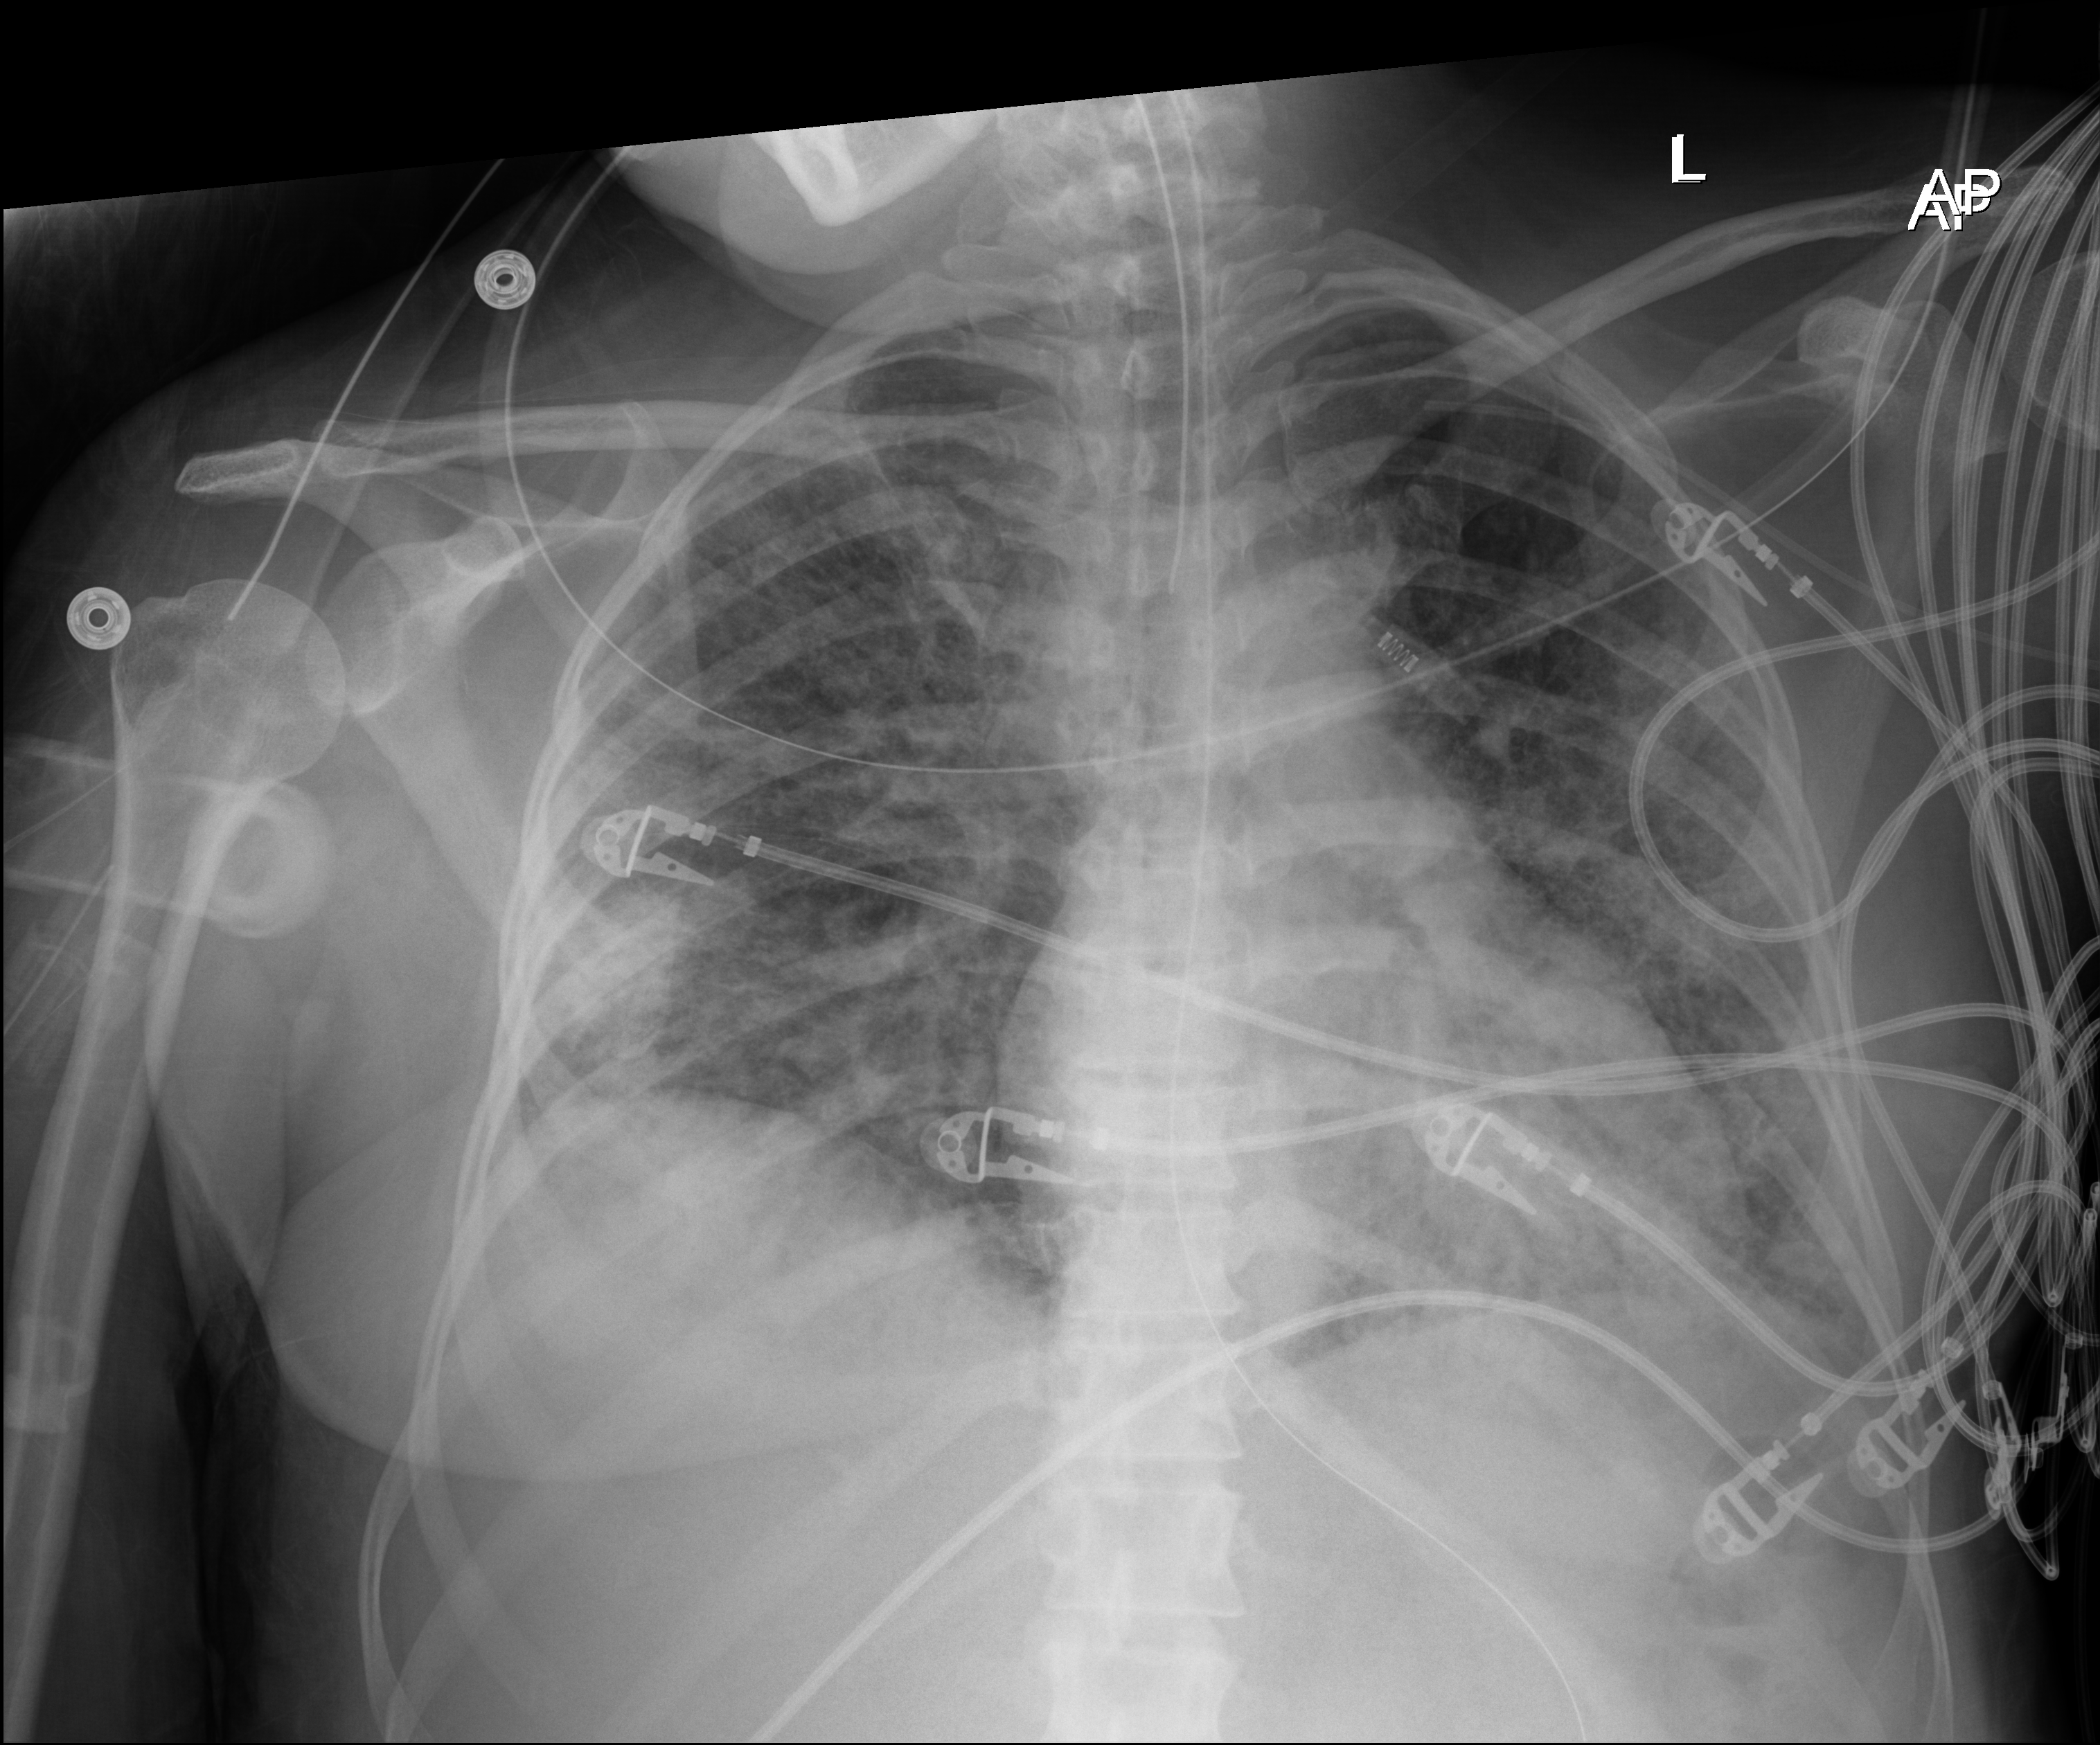
Portable chest radiograph; anteroposterior (AP) projection. Patient hospitalised with COVID-19; female, aged 18–59 years.
Hospital-stay facts (about this admission, not read from this image; timing relative to this image not recorded): admitted to intensive care during this hospital stay: yes; length of hospital stay: 71 days.